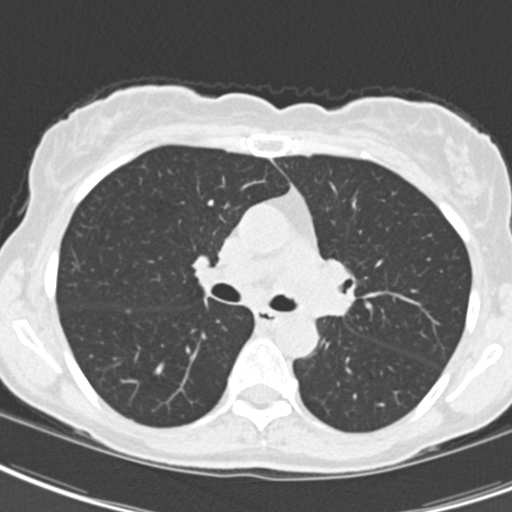
Chest CT (low-dose screening protocol), one axial image, first (baseline) screen, lung window (W 1500 / L -600 HU), 2 mm slice thickness, standard (soft-tissue) reconstruction kernel (B30f), slice 66 of 189 in the series. Female participant, aged 62 years at enrolment.
- Expert reader's lesion annotation, bounding box (x1, y1, x2, y2) in pixels: (296, 246, 372, 329).
- The exam's reader record, not a measurement of the box and not confirmed to be the same lesion: non-calcified nodule or mass ≥4 mm, right upper lobe, 24 × 20 mm, smooth margins, ground glass attenuation.
- Note: the box lies in the patient's left hemithorax on this image, whereas the reader's record names the right lung; they may be different findings.
- Later outcome: lung cancer diagnosed 24 days after this screen — oat cell carcinoma, left hilum, left main stem bronchus, stage IIIB (AJCC 6th edition), 50 mm at pathology.